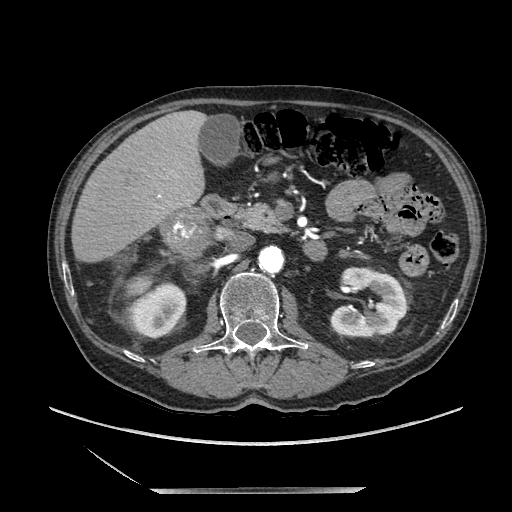
Contrast-enhanced abdominal CT, one axial slice. Position 97 of 243 along the scan axis. Soft-tissue window (W 400 / L 40 HU). 1.25 mm slice thickness. 512 × 512 image matrix, field of view 420 × 420 mm. Male patient. From the clinical record (not read from this slice): diagnosis: adrenocortical carcinoma; tumour side: right adrenal; tumour size at pathology: 16 cm; Ki-67 index: 17 %; stage (as recorded): 3.
Structures marked on this image (semi-automatic segmentation, software-assisted and operator-edited):
- mass: box from (x=165, y=208) to (x=213, y=254) px